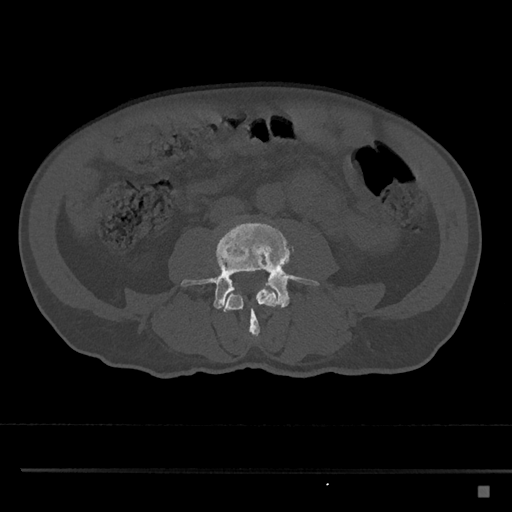
CT including the spine, one axial slice. Slice 660 of 797 in the series (ordered by position). Reconstruction kernel Br40s/3. Bone window (W 1800 / L 400 HU). 0.5 mm slice thickness. 512 × 512 image matrix, field of view 391 × 391 mm. Male patient, age 59 years. Case-level facts recorded for this patient, not image findings: primary cancer: prostate.
Outlined on this slice (semi-automatic segmentation, software-assisted and operator-edited):
- L3 vertebra: box from (x=222, y=284) to (x=282, y=337) px
- L4 vertebra: (x=180, y=221)–(x=319, y=309)